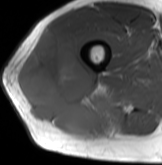
MRI of an extremity soft-tissue mass, one axial slice; position 48 of 61 along the scan axis; MR volume resampled by the dataset authors to the PET/CT grid (not the native acquisition matrix); 162 × 165 image matrix. Male patient. From the clinical record (not read from this slice): histological type: poorly differentiated synovial sarcoma; grade: high; site of the primary tumour: right buttock.
Annotated regions visible in this slice (expert contour drawn on MRI and transferred to this co-registered scan by the dataset authors):
- gross tumour volume including surrounding oedema: bounding box [x1, y1, x2, y2] px = [20, 31, 115, 135]
- gross tumour volume (mass): [20, 31, 115, 135]